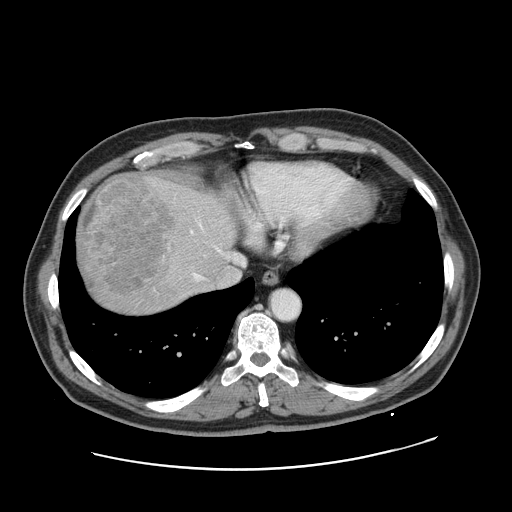
Contrast-enhanced abdominal CT, one axial slice. Position 143 of 178 along the scan axis. 120 kVp. Soft-tissue window (W 400 / L 40 HU). 2.5 mm slice thickness. 512 × 512 image matrix. Male patient, age 63 years. From the clinical record (not read from this slice): diagnosis: colorectal cancer liver metastases, imaged before liver resection; multiple liver metastases: yes; largest metastasis: 8 cm; chemotherapy before resection: no.
Outlined on this slice (expert manual segmentation):
- hepatic veins: box from (x=191, y=225) to (x=245, y=279) px
- liver: (x=77, y=172)–(x=237, y=315)
- planned liver remnant (the part of the liver to remain after resection): (x=182, y=186)–(x=238, y=270)
- liver metastasis: (x=79, y=176)–(x=170, y=292)